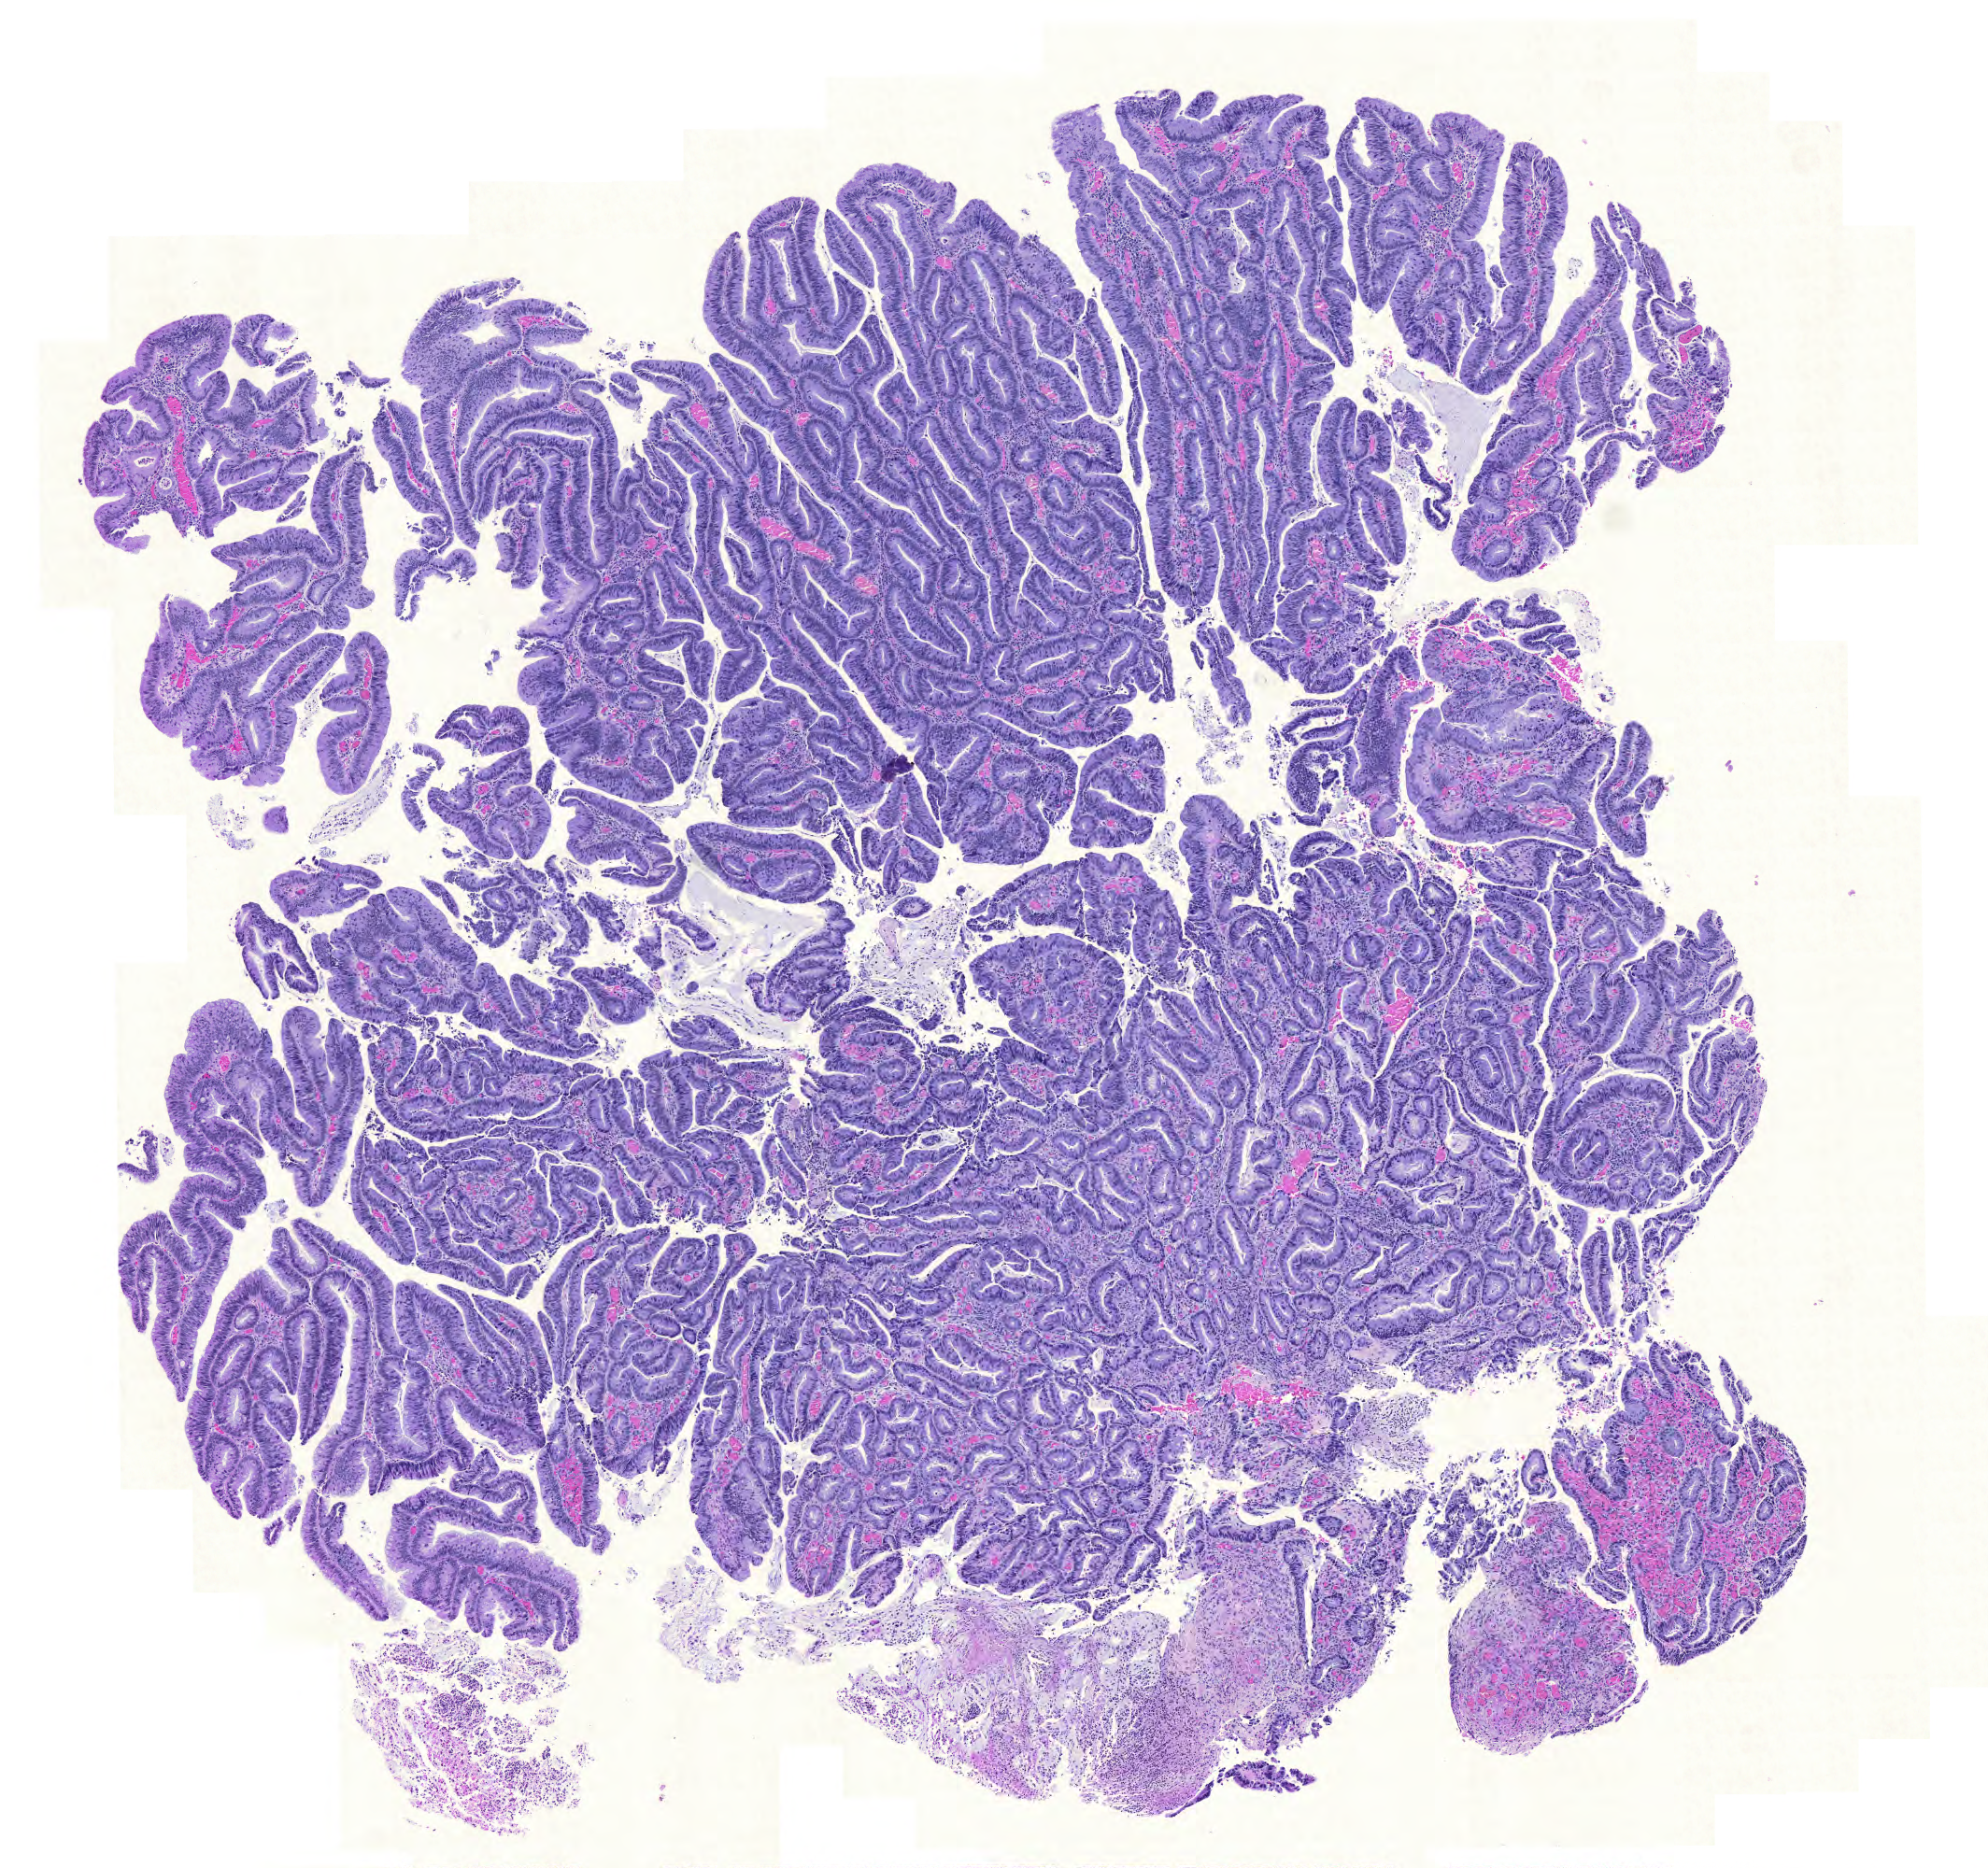
Whole-slide histology image, H&E-stained — low-resolution overview of the scanned area, about 7.9 x 7.4 mm. FFPE section. Rectum, primary tumour sample. Male, age 72 years at initial diagnosis.
Diagnosis: Adenocarcinoma, NOS (rectosigmoid junction). AJCC pathologic stage: IIA.